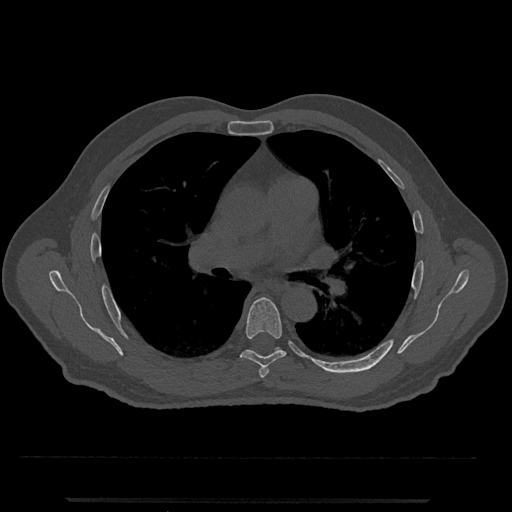
CT including the spine, one axial slice; reconstruction kernel Br40s/3; 120 kVp; bone window (W 1800 / L 400 HU); 512 × 512 image matrix, field of view 419 × 419 mm. Patient: male, 63 years. Case-level facts recorded for this patient, not image findings: primary cancer: prostate.
Outlined on this slice (semi-automatically segmented with operator editing):
- T5 vertebra: box from (x=259, y=365) to (x=269, y=378) px
- T6 vertebra: (x=240, y=297)–(x=286, y=367)
- T7 vertebra: (x=275, y=347)–(x=278, y=350)